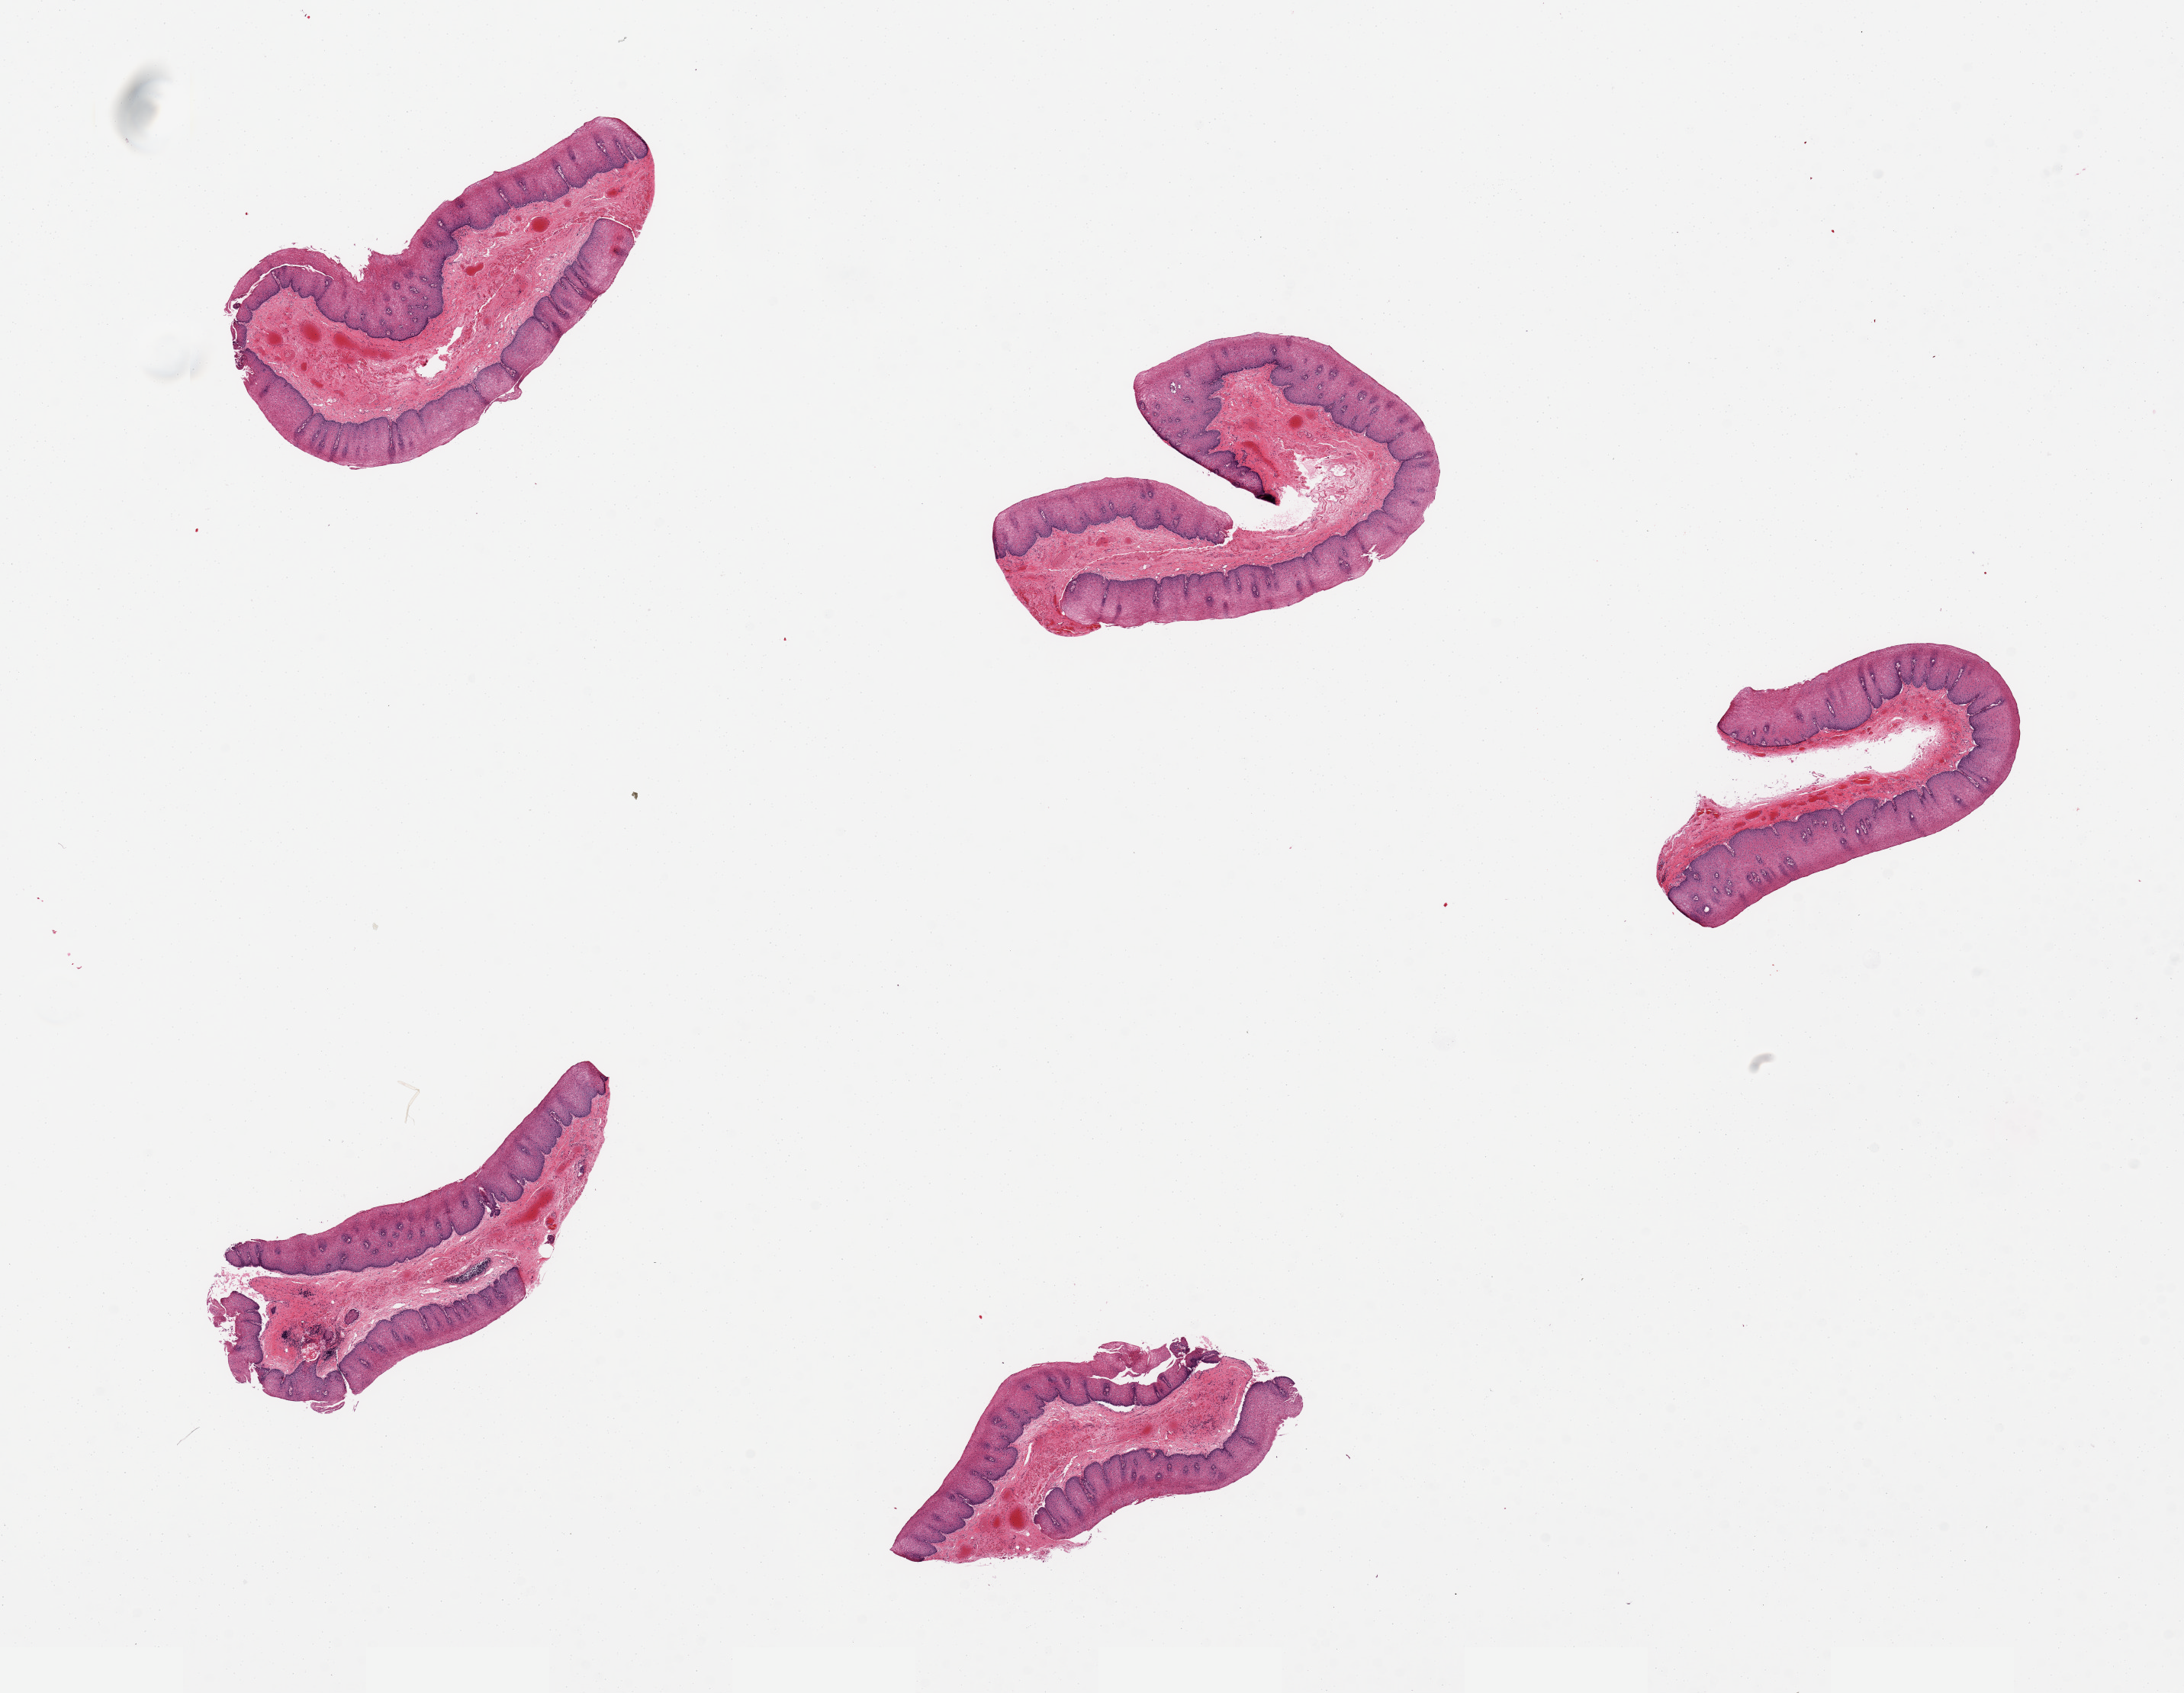
Digitized hematoxylin and eosin (H&E)-stained section — shown as a low-resolution overview of the whole scanned area (about 22.6 x 17.6 mm). PAXgene-fixed paraffin-embedded (PFPE) section. Section of esophageal mucous membrane (target tissue). Donor tissue sample. Donor: male.
Pathologist's review note for this sample: 5 pieces.